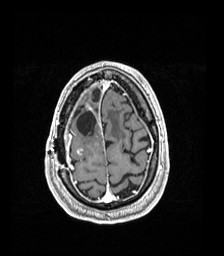
Brain MRI from a brain-tumour surgery series, one axial slice. Slice 36 of 192 in the series (ordered by position). T1-weighted post-contrast. 1 mm slice thickness. 224 × 256 image matrix. Case-level facts recorded for this patient, not image findings: histopathology: Astrocytoma; WHO grade: 4; IDH mutation: yes; tumour location: Right Frontal.
Structures marked on this image (outlined manually by an expert reader):
- previous resection cavity: bounding box (x1, y1, x2, y2) in pixels: (76, 110, 96, 135)
- tumour: (76, 146, 85, 156)